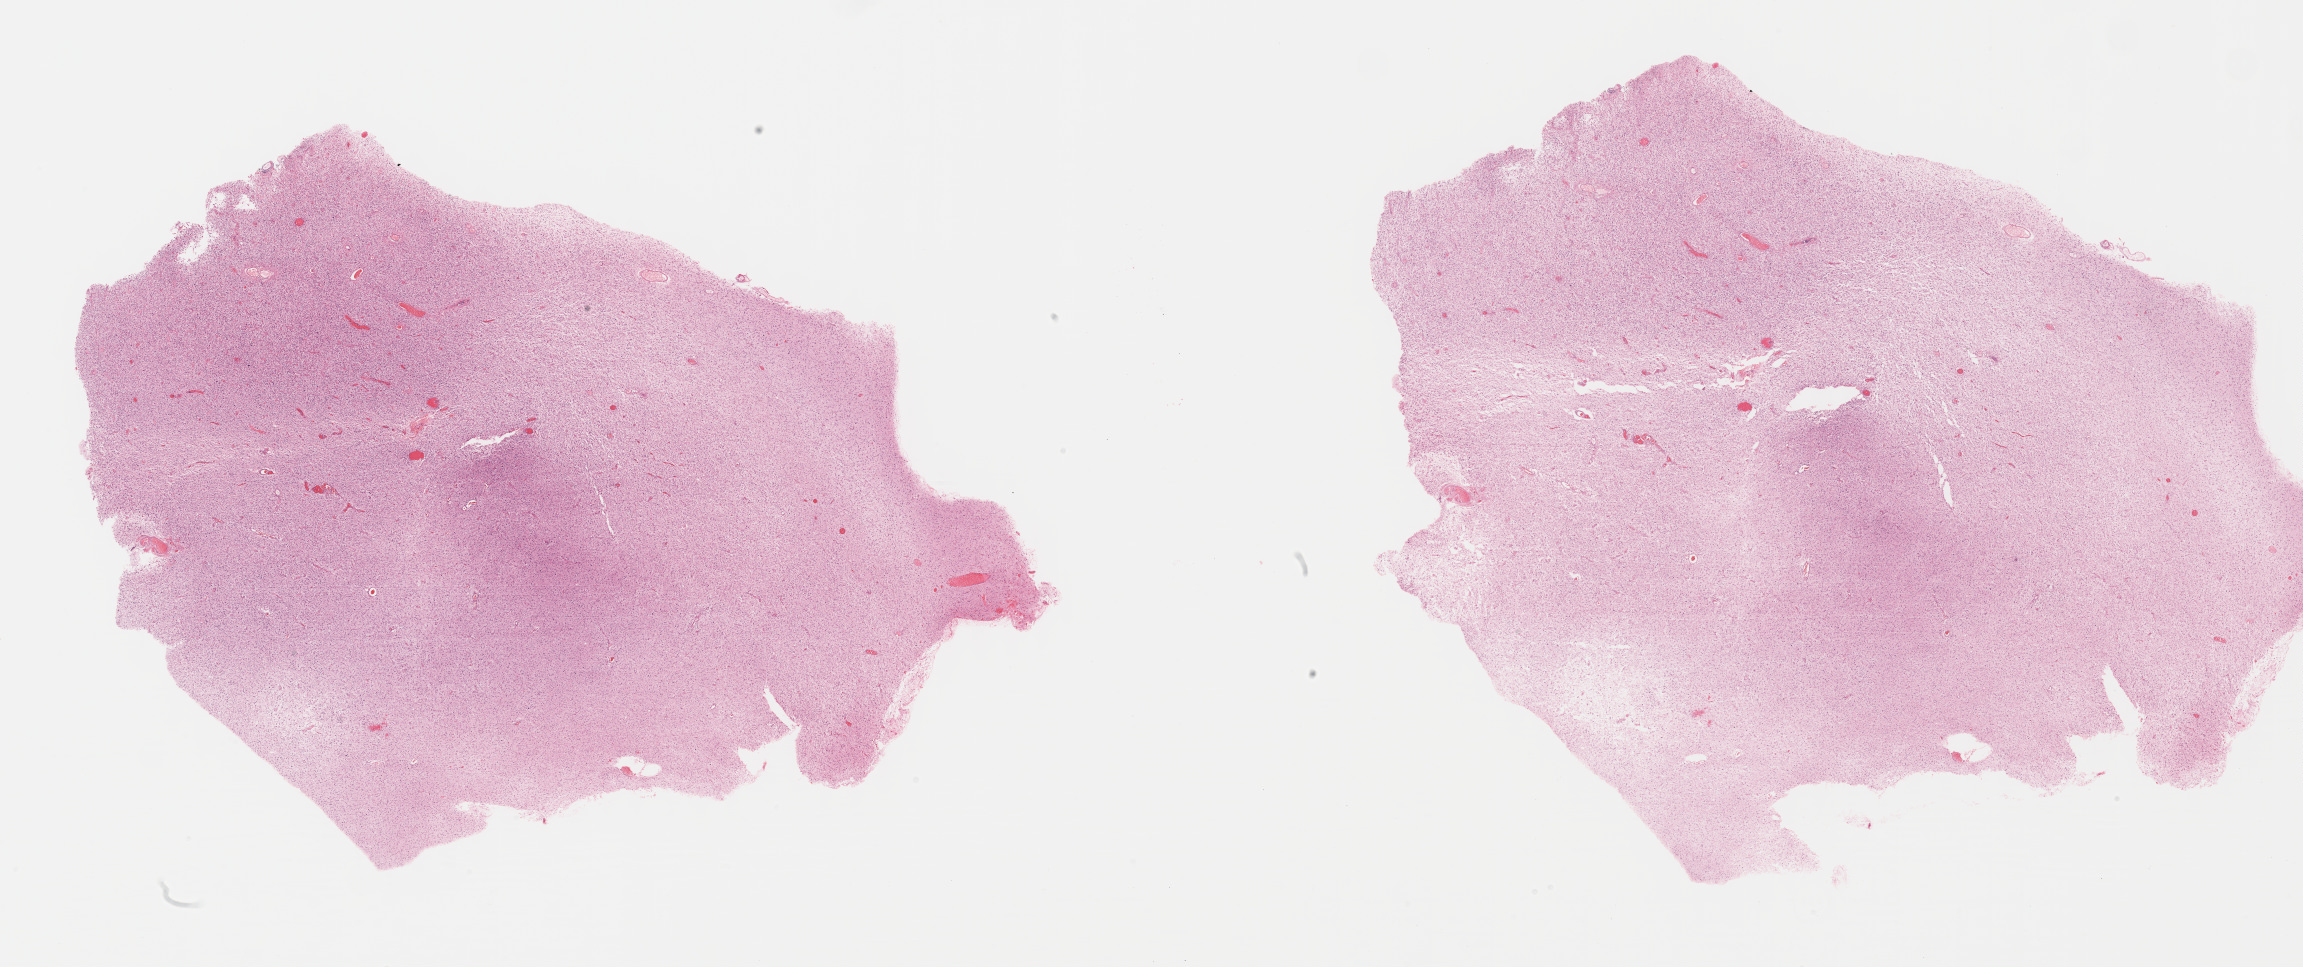
Hematoxylin and eosin (H&E) stained whole-slide image, shown as a low-resolution overview of the whole scanned area (about 37.2 x 15.6 mm, slide scanned at 40x); formalin-fixed paraffin-embedded (FFPE) diagnostic section; primary tumour sample from the brain. Patient: male, age at initial diagnosis 40 years.
Pathologic diagnosis: Glioblastoma.